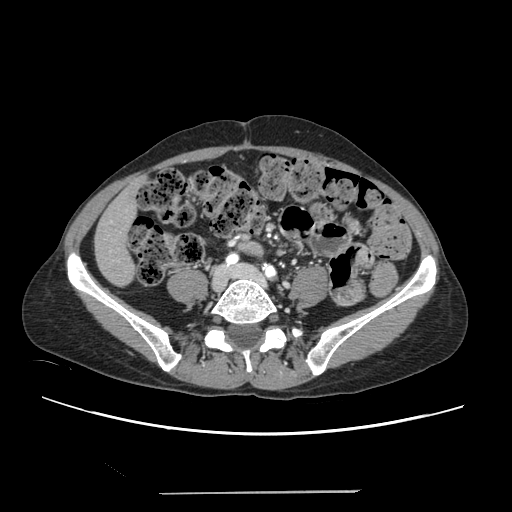
Contrast-enhanced abdominal CT, one axial slice. 120 kVp. Intravenous contrast given. Soft-tissue window (W 400 / L 40 HU). 1.25 mm slice thickness. 512 × 512 image matrix, field of view 371 × 371 mm. Female patient, age 60 years. Case-level facts recorded for this patient, not image findings: diagnosis: colorectal cancer liver metastases, imaged before liver resection; multiple liver metastases: no; largest metastasis: 1.5 cm; disease in both lobes: no.
Structures marked on this image (manually delineated by an expert):
- liver: bounding box [x1, y1, x2, y2] px = [96, 183, 138, 284]
- planned liver remnant (the part of the liver to remain after resection): [96, 182, 138, 285]
- portal vein (with intrahepatic branches): [110, 220, 112, 252]